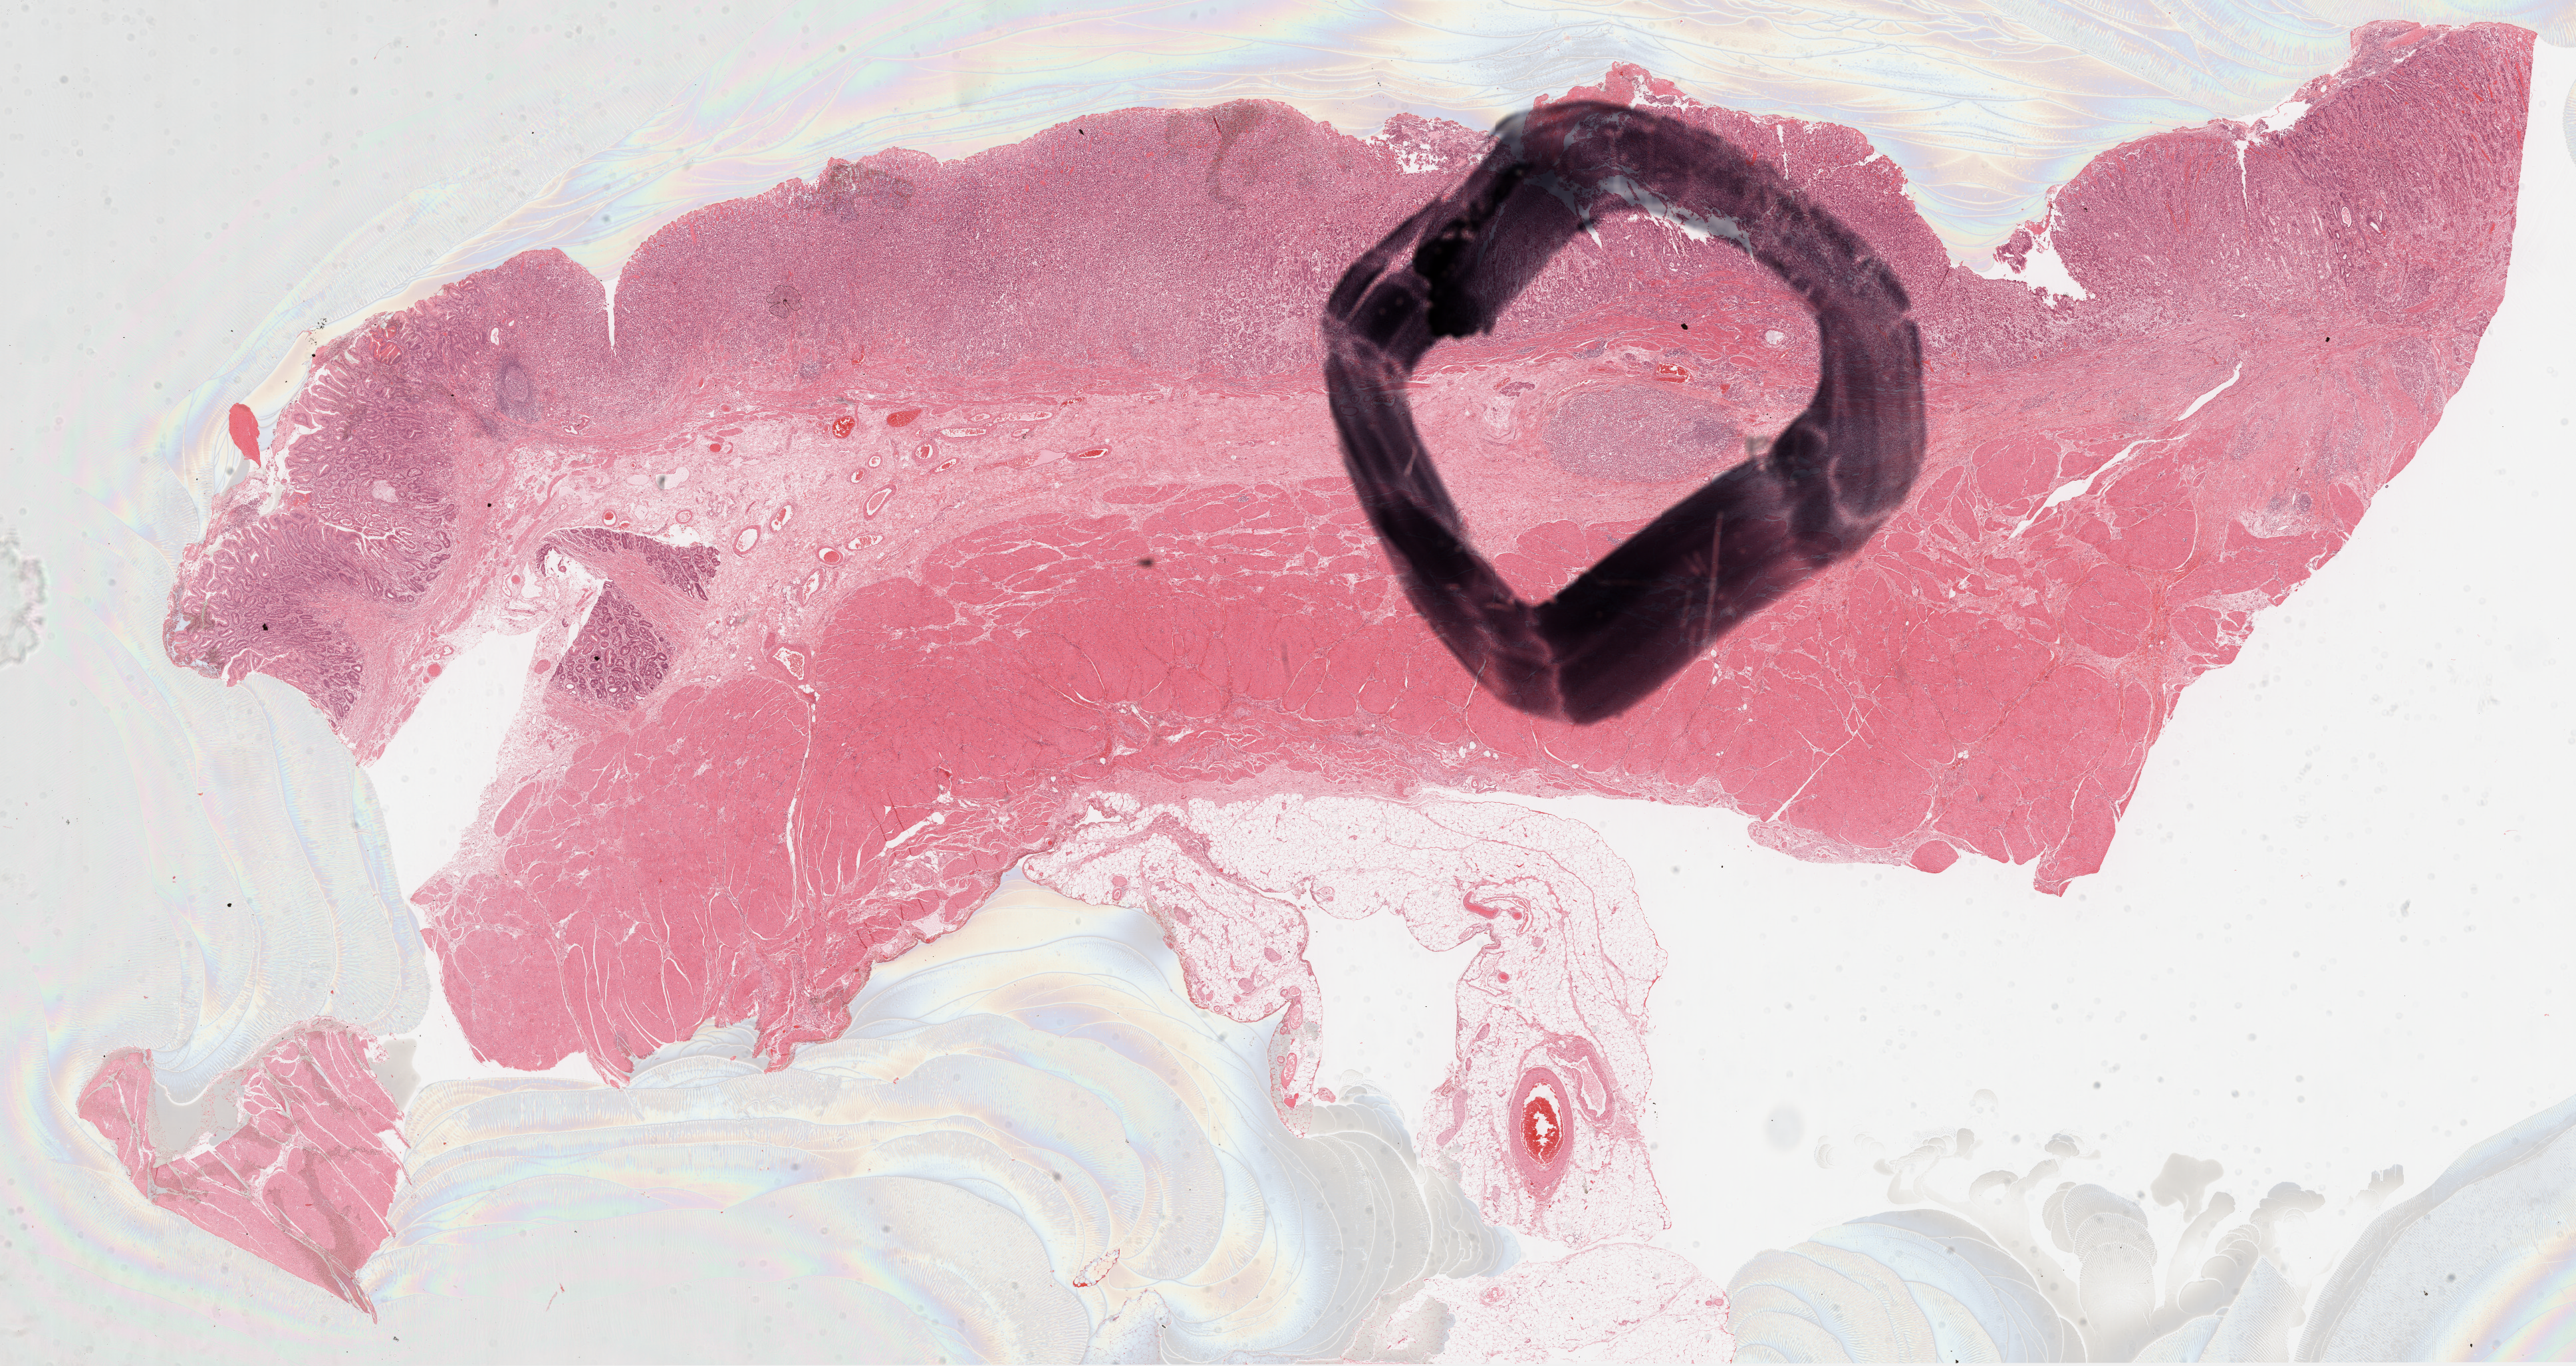
H&E-stained whole-slide image — shown as a low-resolution overview of the whole scanned area (about 31.0 x 16.4 mm). Formalin-fixed paraffin-embedded (FFPE) diagnostic section. Sample: primary tumour, stomach. Male, age 82 years at initial diagnosis. Histologic grade: G3 (poorly differentiated).
Diagnosis: Carcinoma, diffuse type (fundus of stomach). AJCC pathologic stage: IB (6th edition). Lymph nodes positive (case pathology): 0 of 23 examined.